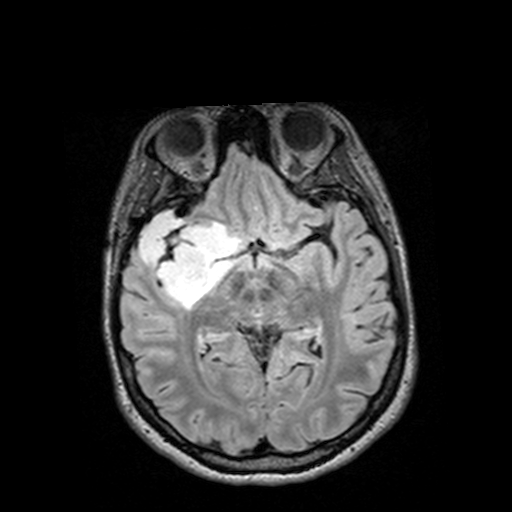
Brain MRI from a brain-tumour surgery series, one axial slice. Slice 79 of 144 in the series (ordered by position). T2 FLAIR. 1 mm slice thickness. 512 × 512 image matrix, field of view 250 × 250 mm. From the clinical record (not read from this slice): histopathology: Astrocytoma; WHO grade: 3.
Structures marked on this image (expert manual segmentation):
- tumour: bounding box (x1, y1, x2, y2) in pixels: (126, 213, 232, 307)